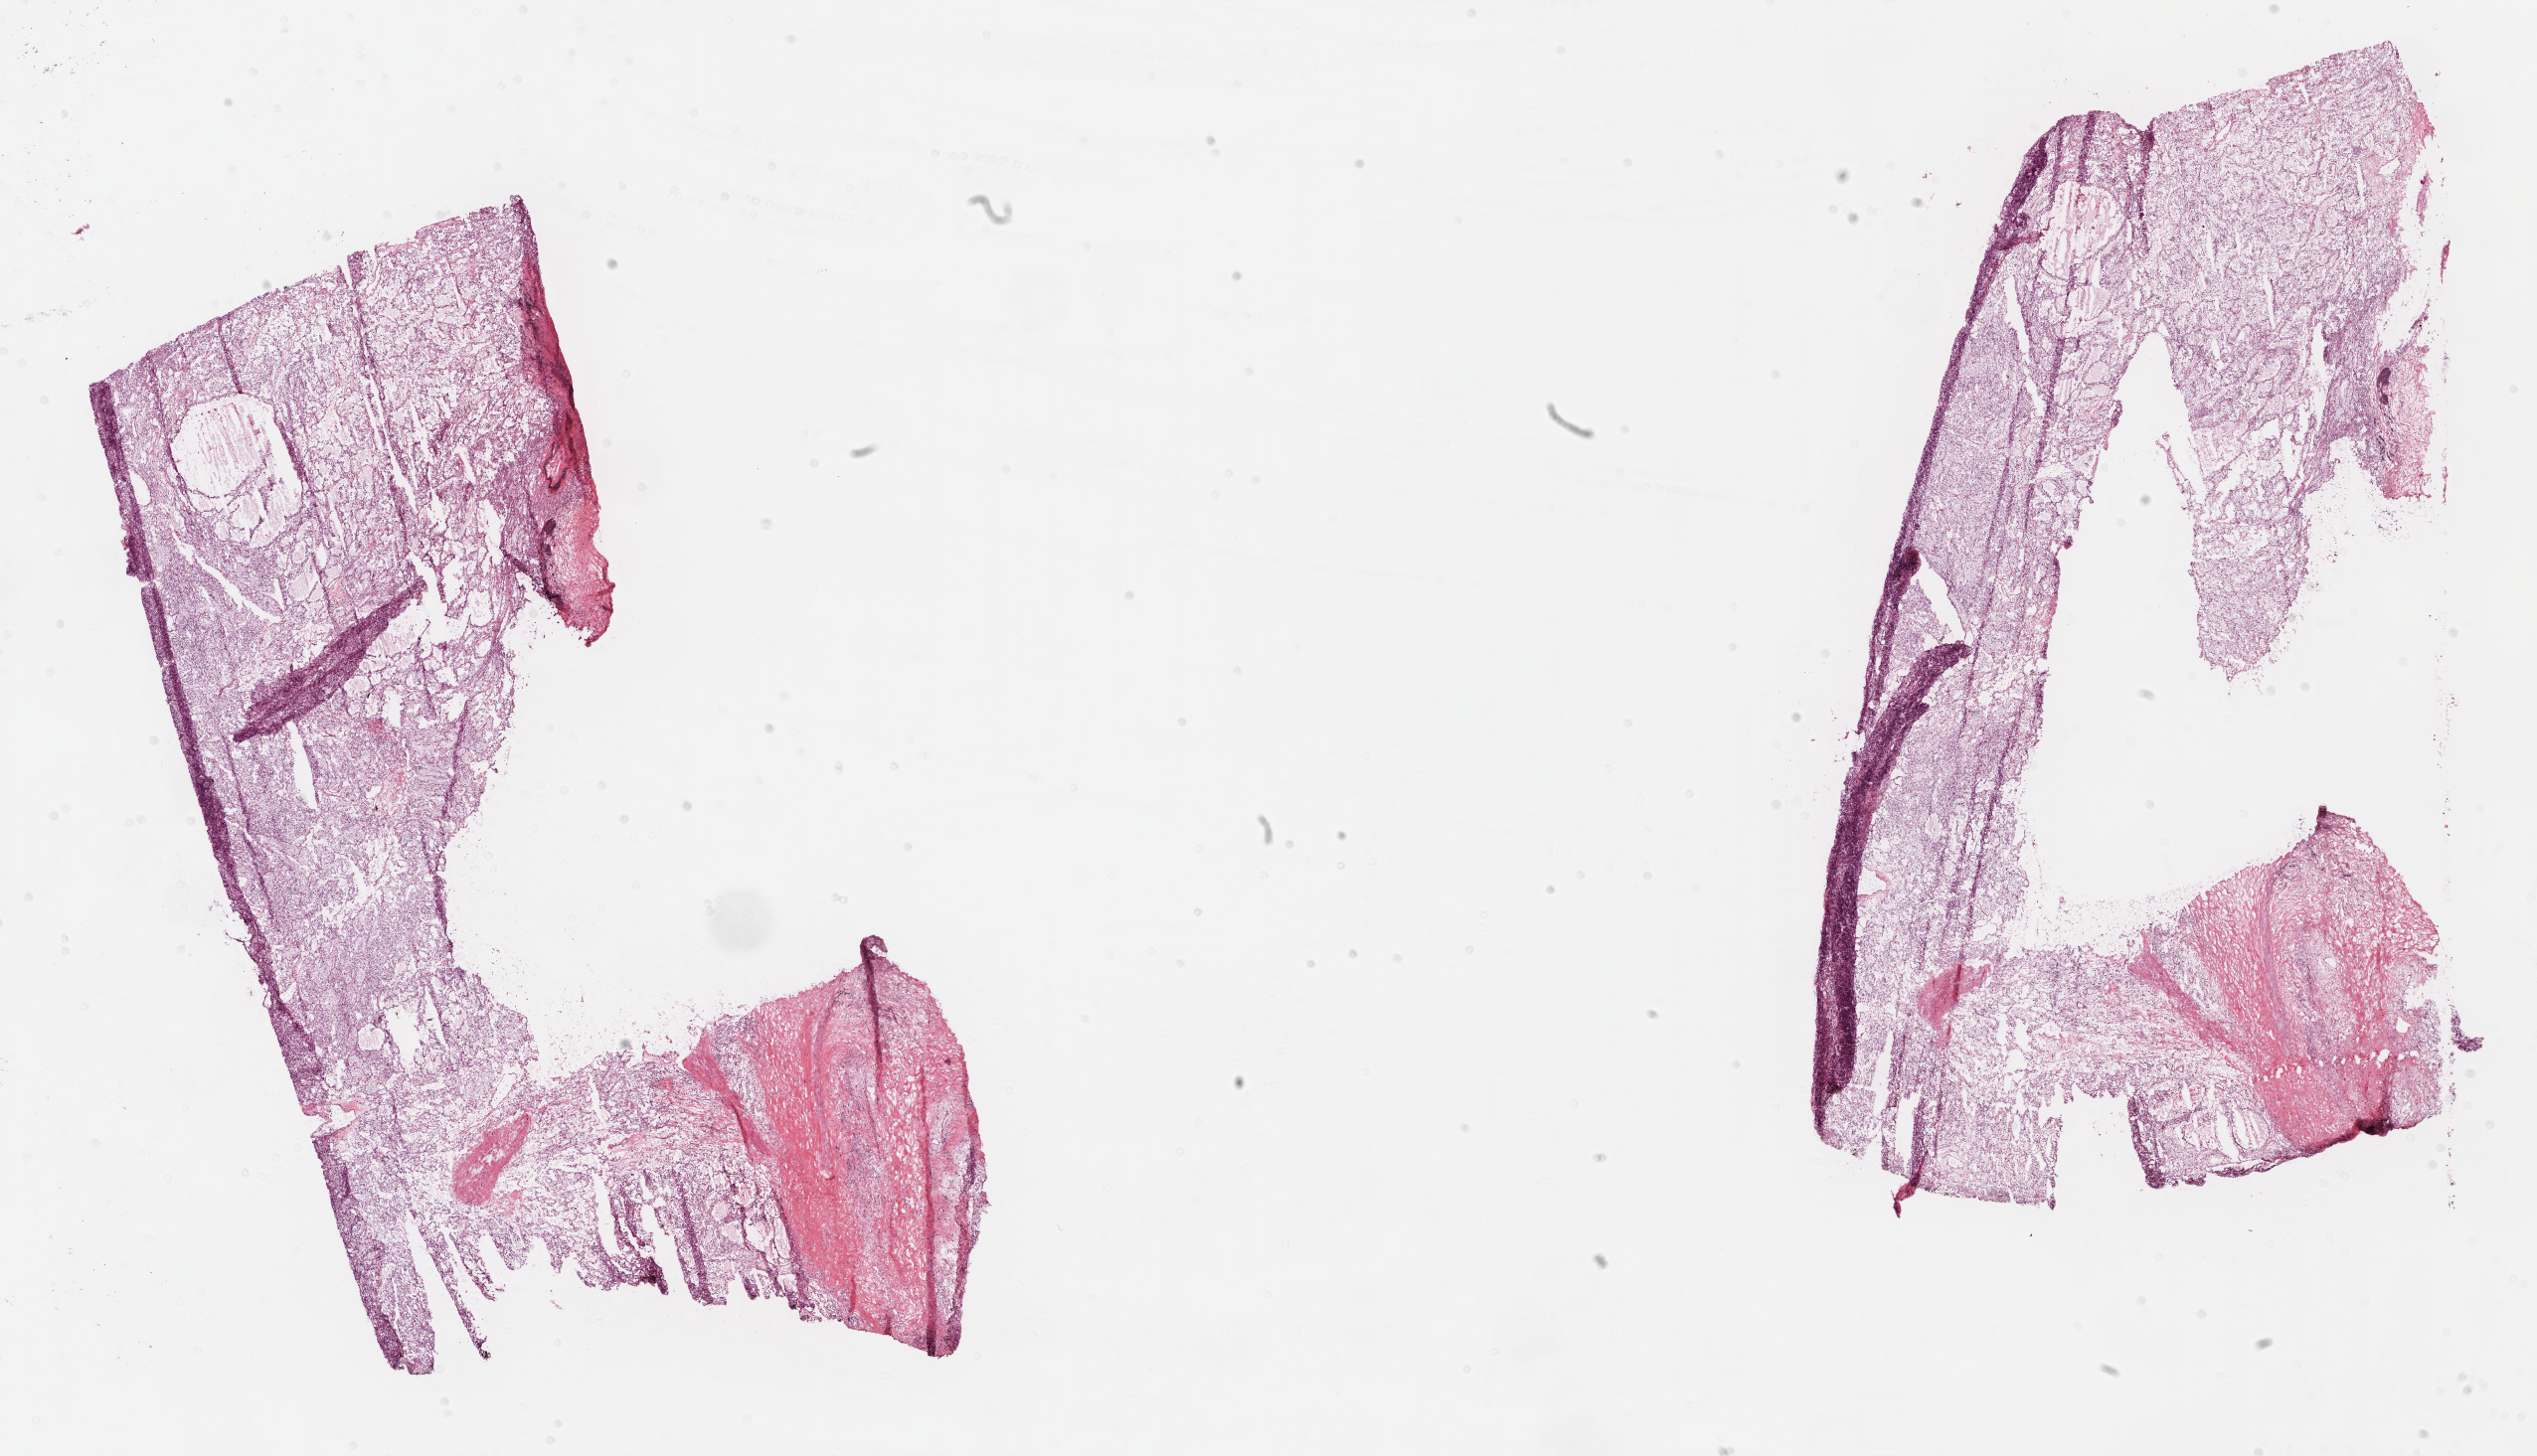
Digitized Hematoxylin and eosin (H&E) stained tissue section (whole slide) — a low-resolution overview of the entire scanned area, about 20.6 x 11.8 mm (slide scanned at 40x), frozen section from the bottom of the tissue portion, sample: primary tumour, kidney. Patient: male, age at initial diagnosis 56 years. Histologic grade: G2 (moderately differentiated). Composition of this section per pathologist review: tumour cells 85%, tumour nuclei 80%, normal cells 0%, stromal cells 15%, necrosis 0%.
Pathologic diagnosis: Clear cell adenocarcinoma, NOS. AJCC pathologic stage: I. Laterality: right.